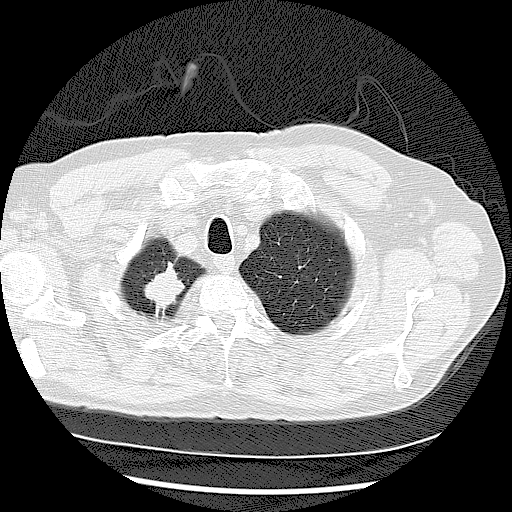
Low-dose screening chest CT, one axial slice; slice 104 of 122 in the series (ordered by position); reconstruction kernel LUNG; lung window (W 1500 / L -600 HU); 2.5 mm slice thickness; 512 × 512 image matrix, field of view 360 × 360 mm.
Outlined on this slice (expert manual segmentation):
- lesion 2 (tumor, upper lobe of right lung): bounding box [x1, y1, x2, y2] px = [144, 263, 184, 310]